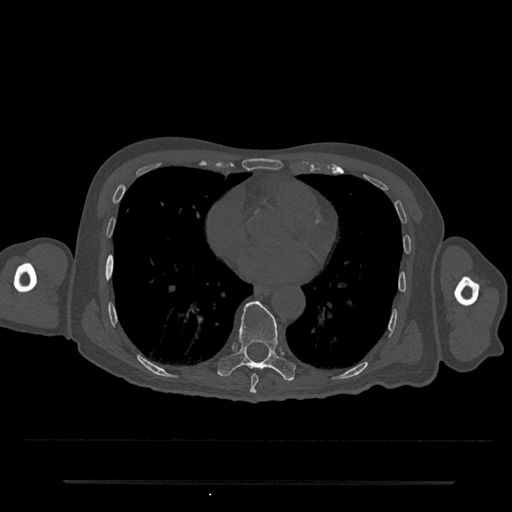
CT including the spine, one axial slice. Slice 378 of 797 in the series (ordered by position). Reconstruction kernel Br40s/3. Bone window (W 1800 / L 400 HU). 512 × 512 image matrix. Male patient, age 74 years. Case-level facts recorded for this patient, not image findings: primary cancer: prostate.
Outlined on this slice (semi-automatically segmented with operator editing):
- T8 vertebra: bounding box (x1, y1, x2, y2) in pixels: (250, 374, 259, 394)
- T9 vertebra: (218, 301, 296, 381)